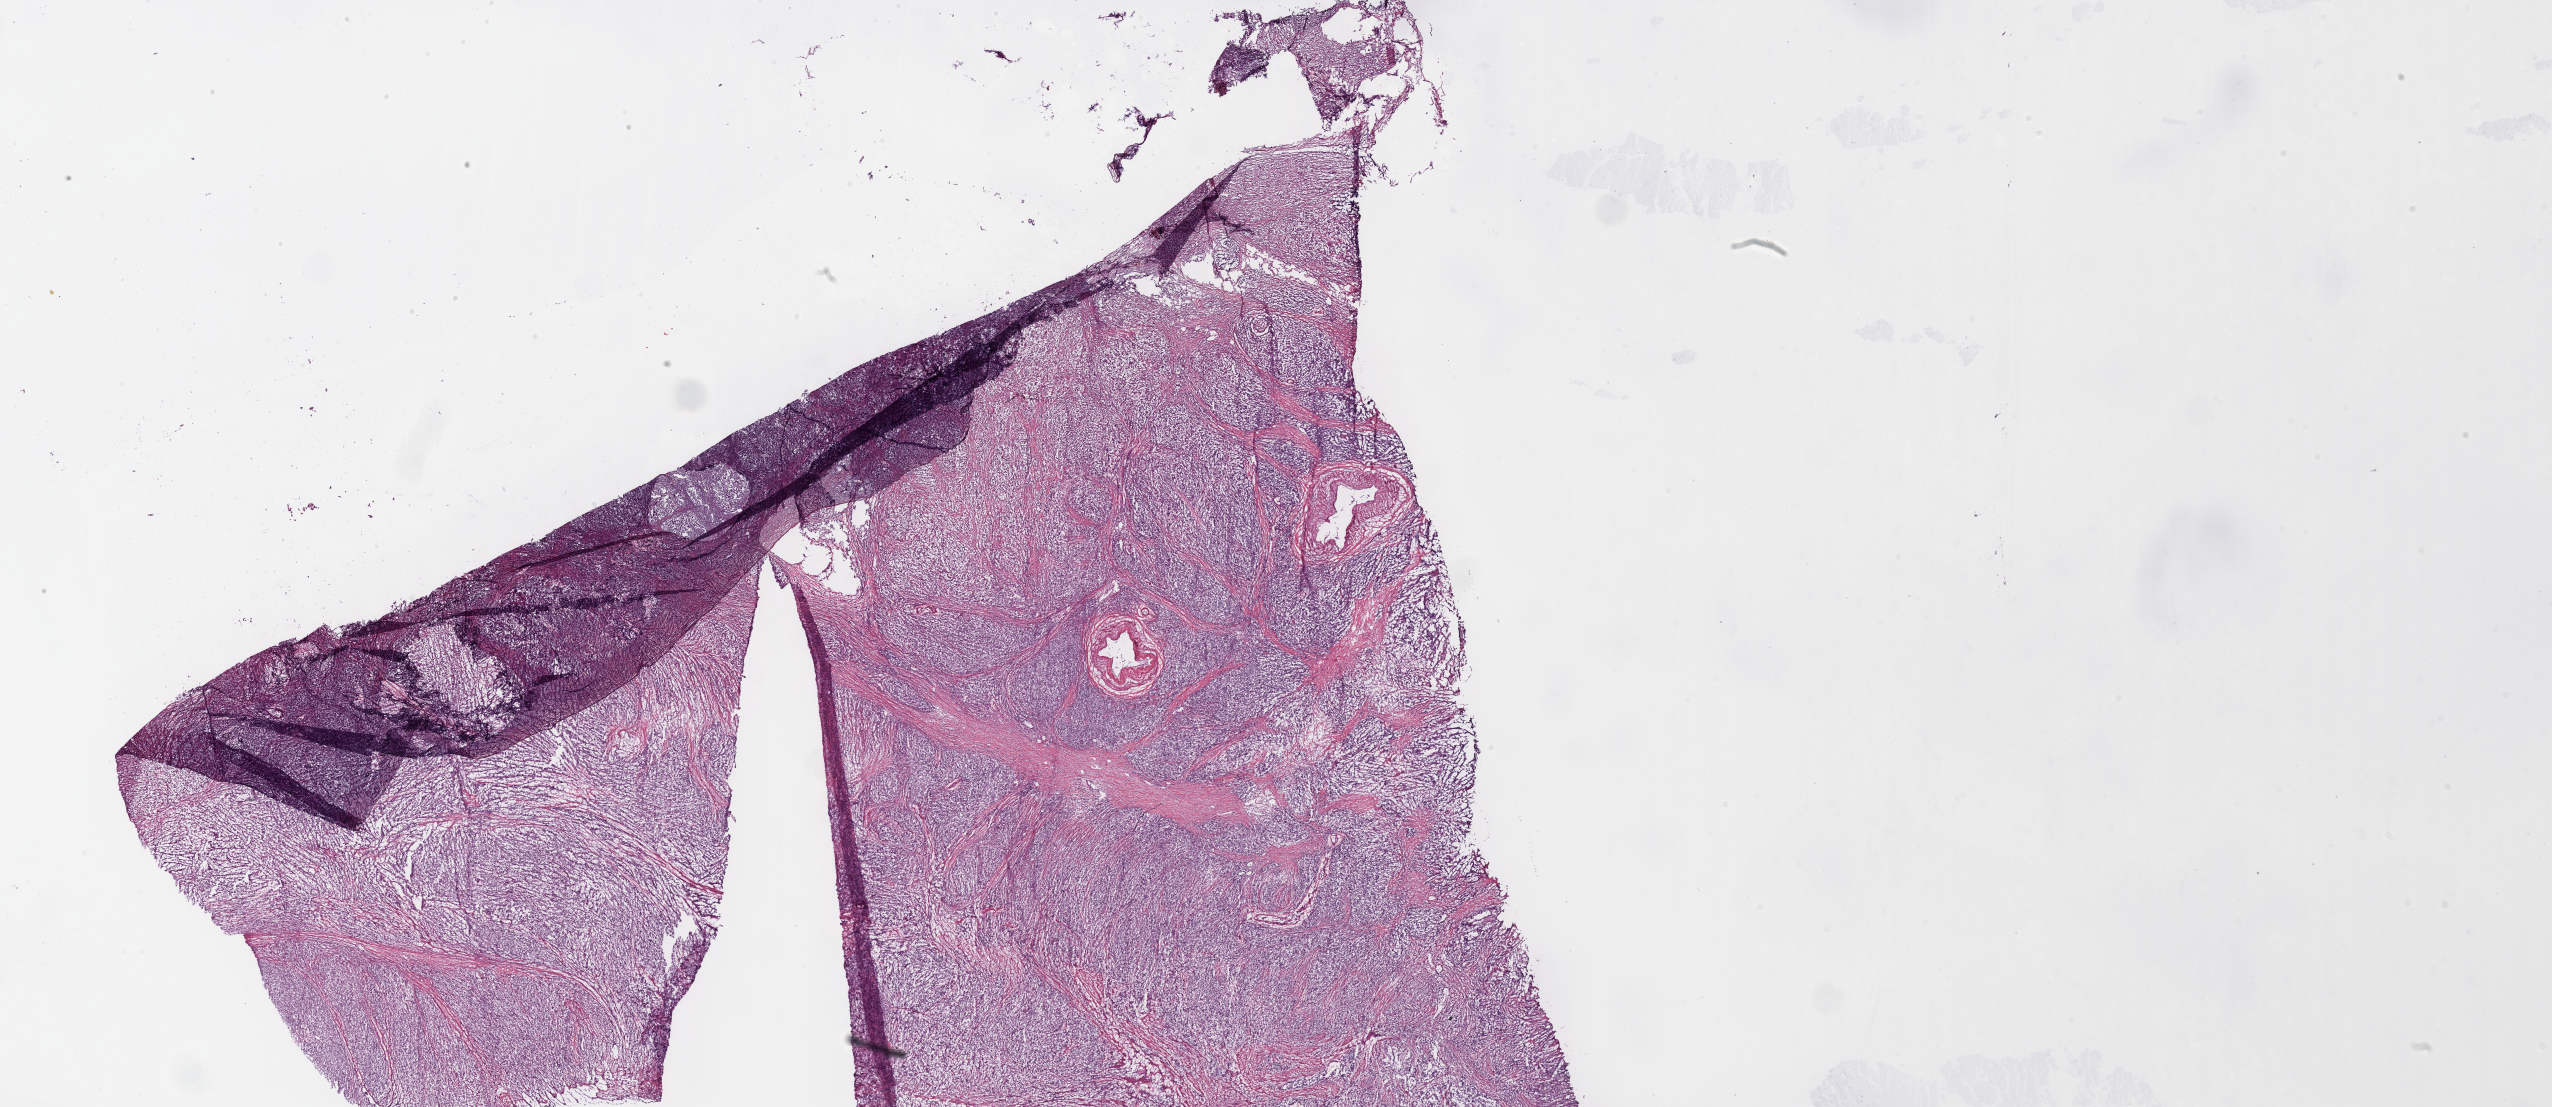
H&E-stained whole-slide image, a low-resolution overview of the entire scanned area, about 40.1 x 17.4 mm. Frozen section. Primary tumour sample from the stomach. Patient: female, age at initial diagnosis 57 years. Histologic grade: G3 (poorly differentiated). Pathologist review of this section (percent, as recorded): tumour cells 92%, tumour nuclei 80%, normal cells 0%, stromal cells 8%, necrosis 0%.
AJCC pathologic stage: IIIC (7th edition). Pathologic diagnosis: Adenocarcinoma, intestinal type. TNM: T4a N3a M0.